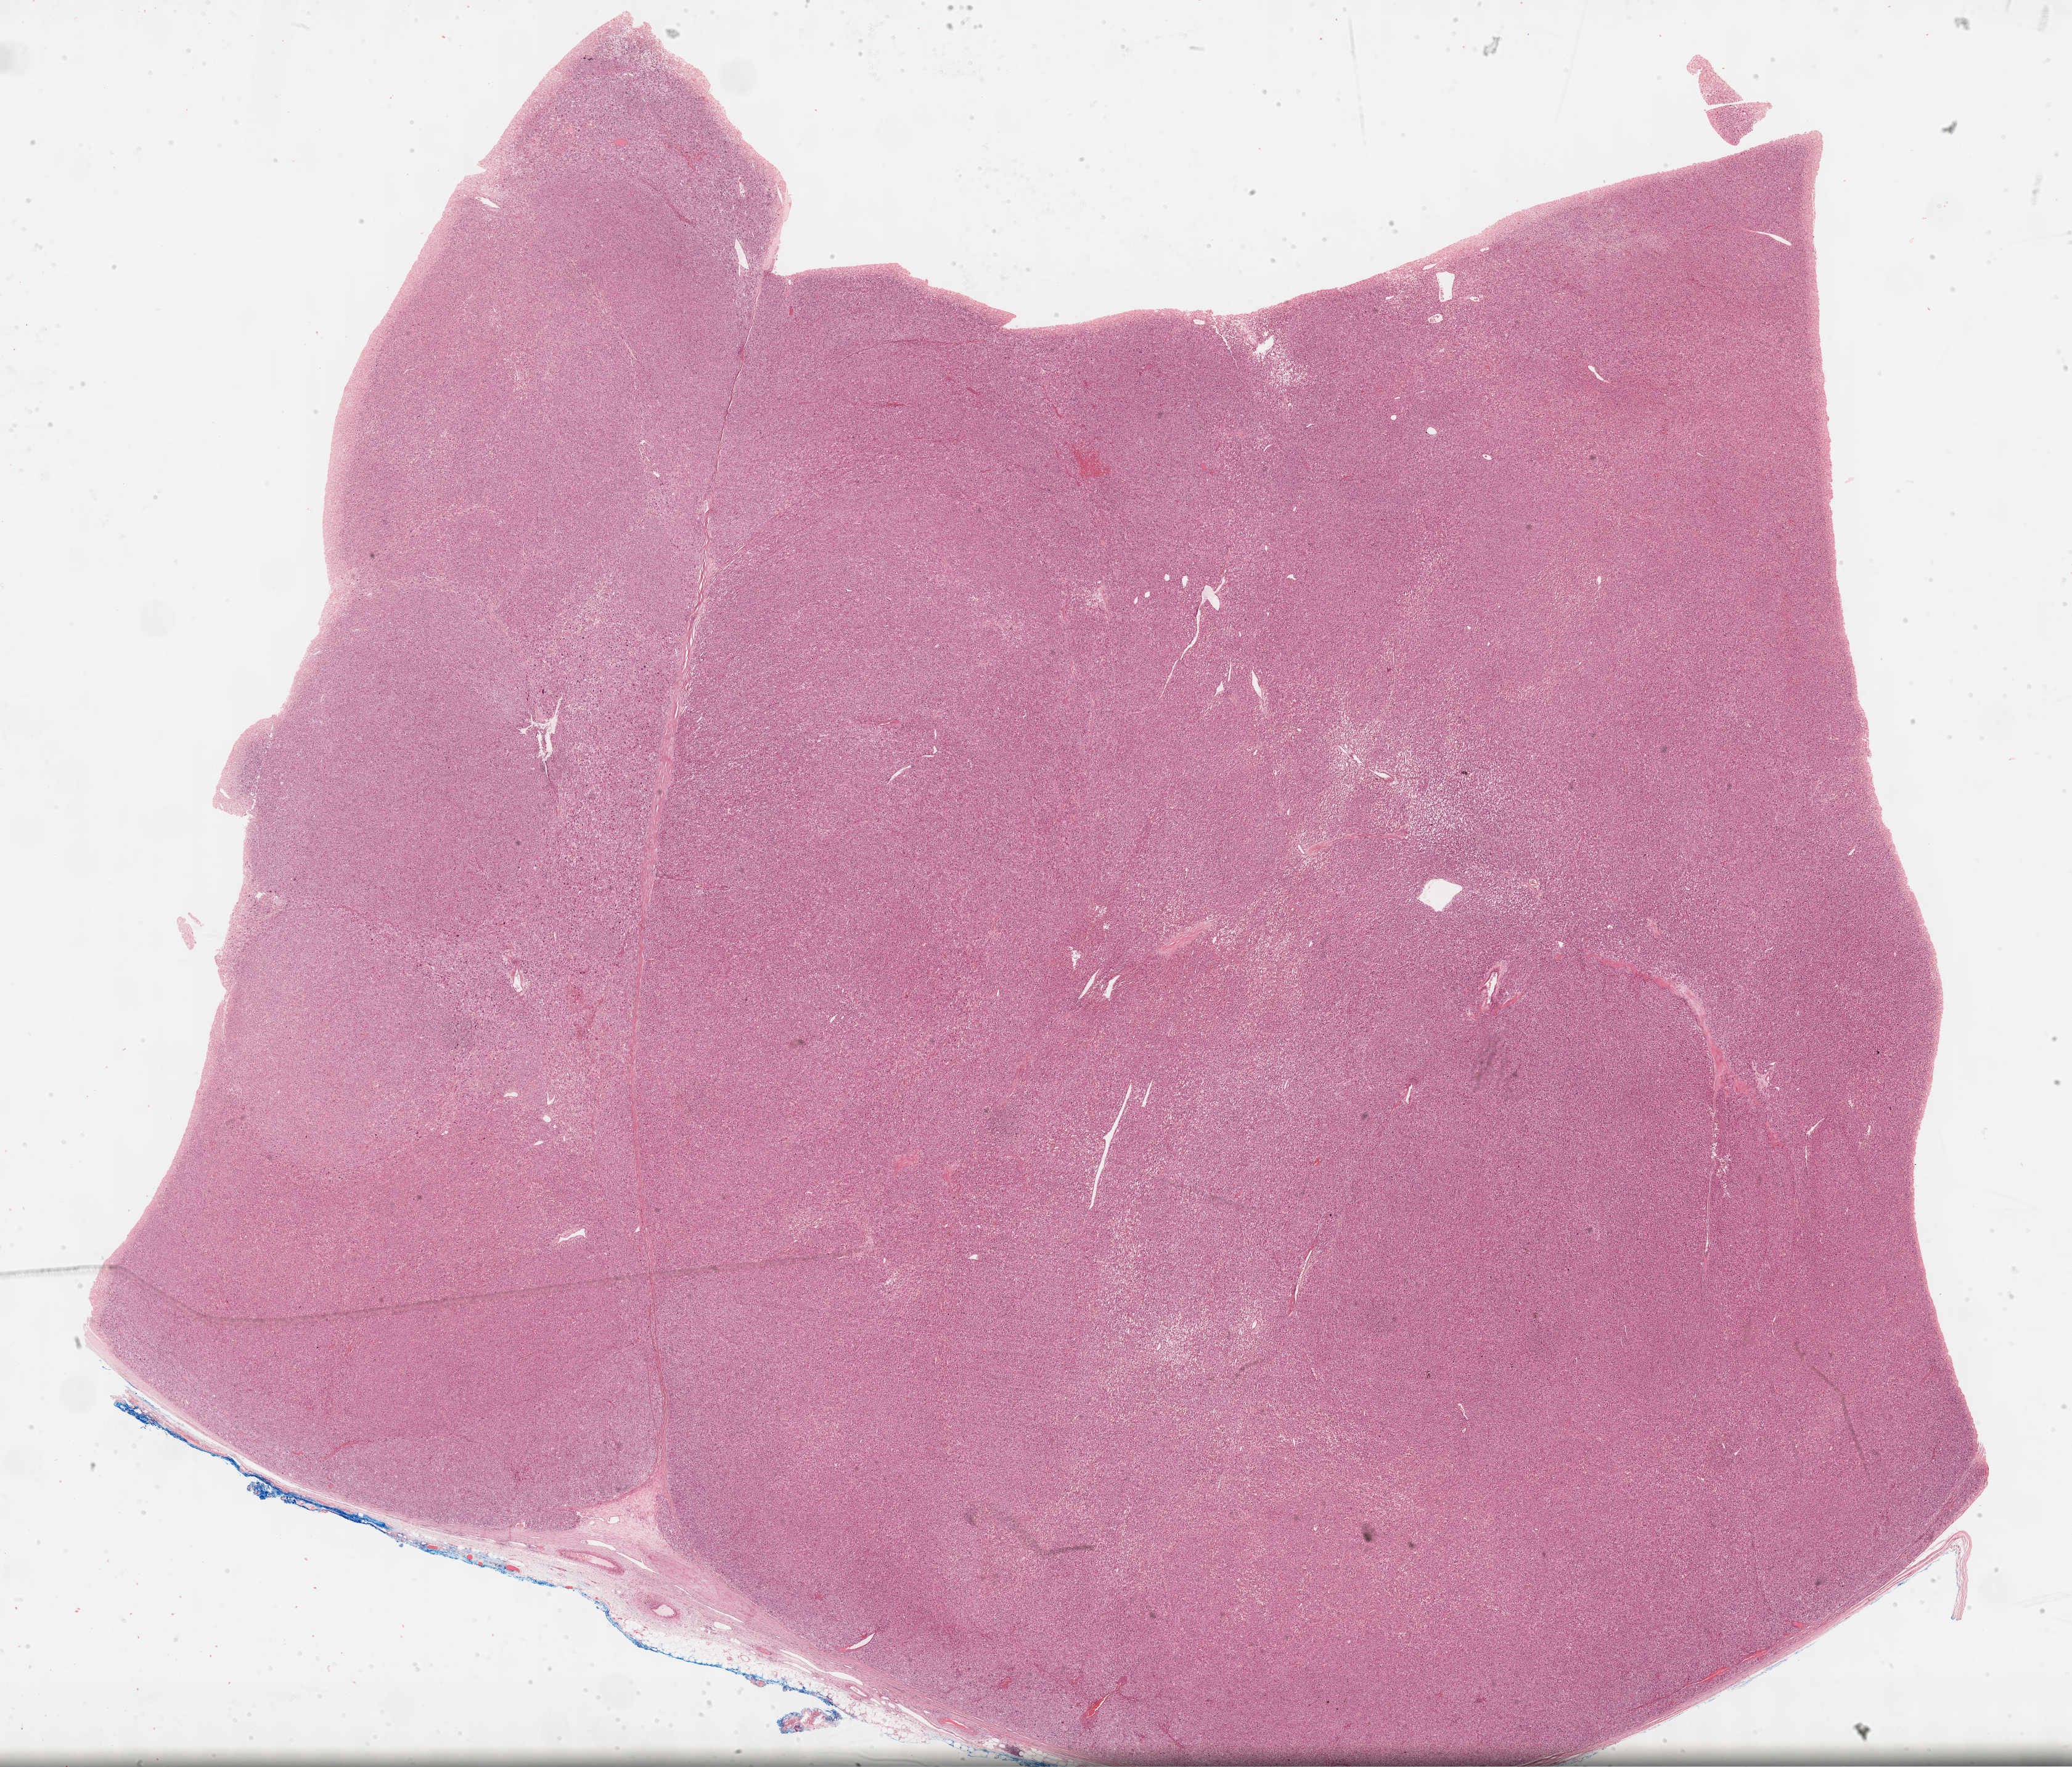
Digitized H&E-stained tissue section (whole slide), low-resolution overview of the scanned area, about 27.2 x 23.2 mm. Formalin-fixed paraffin-embedded (FFPE) diagnostic section. Primary tumour sample from the adrenal cortex. Patient: male, age at initial diagnosis 45 years.
• pathologic diagnosis: Adrenal cortical carcinoma (cortex of adrenal gland)